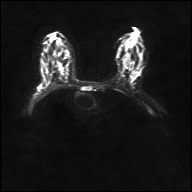
Breast MRI, one axial slice; position 20 of 36 along the scan axis; diffusion-weighted series; image 2 of 4 stored at this slice position (different b-values; order by instance number); 1.5 T; 4 mm slice thickness; 192 × 192 image matrix. Female patient.
Outlined on this slice (expert manual segmentation):
- tumour on diffusion-weighted imaging: bounding box [x1, y1, x2, y2] px = [39, 83, 43, 88]